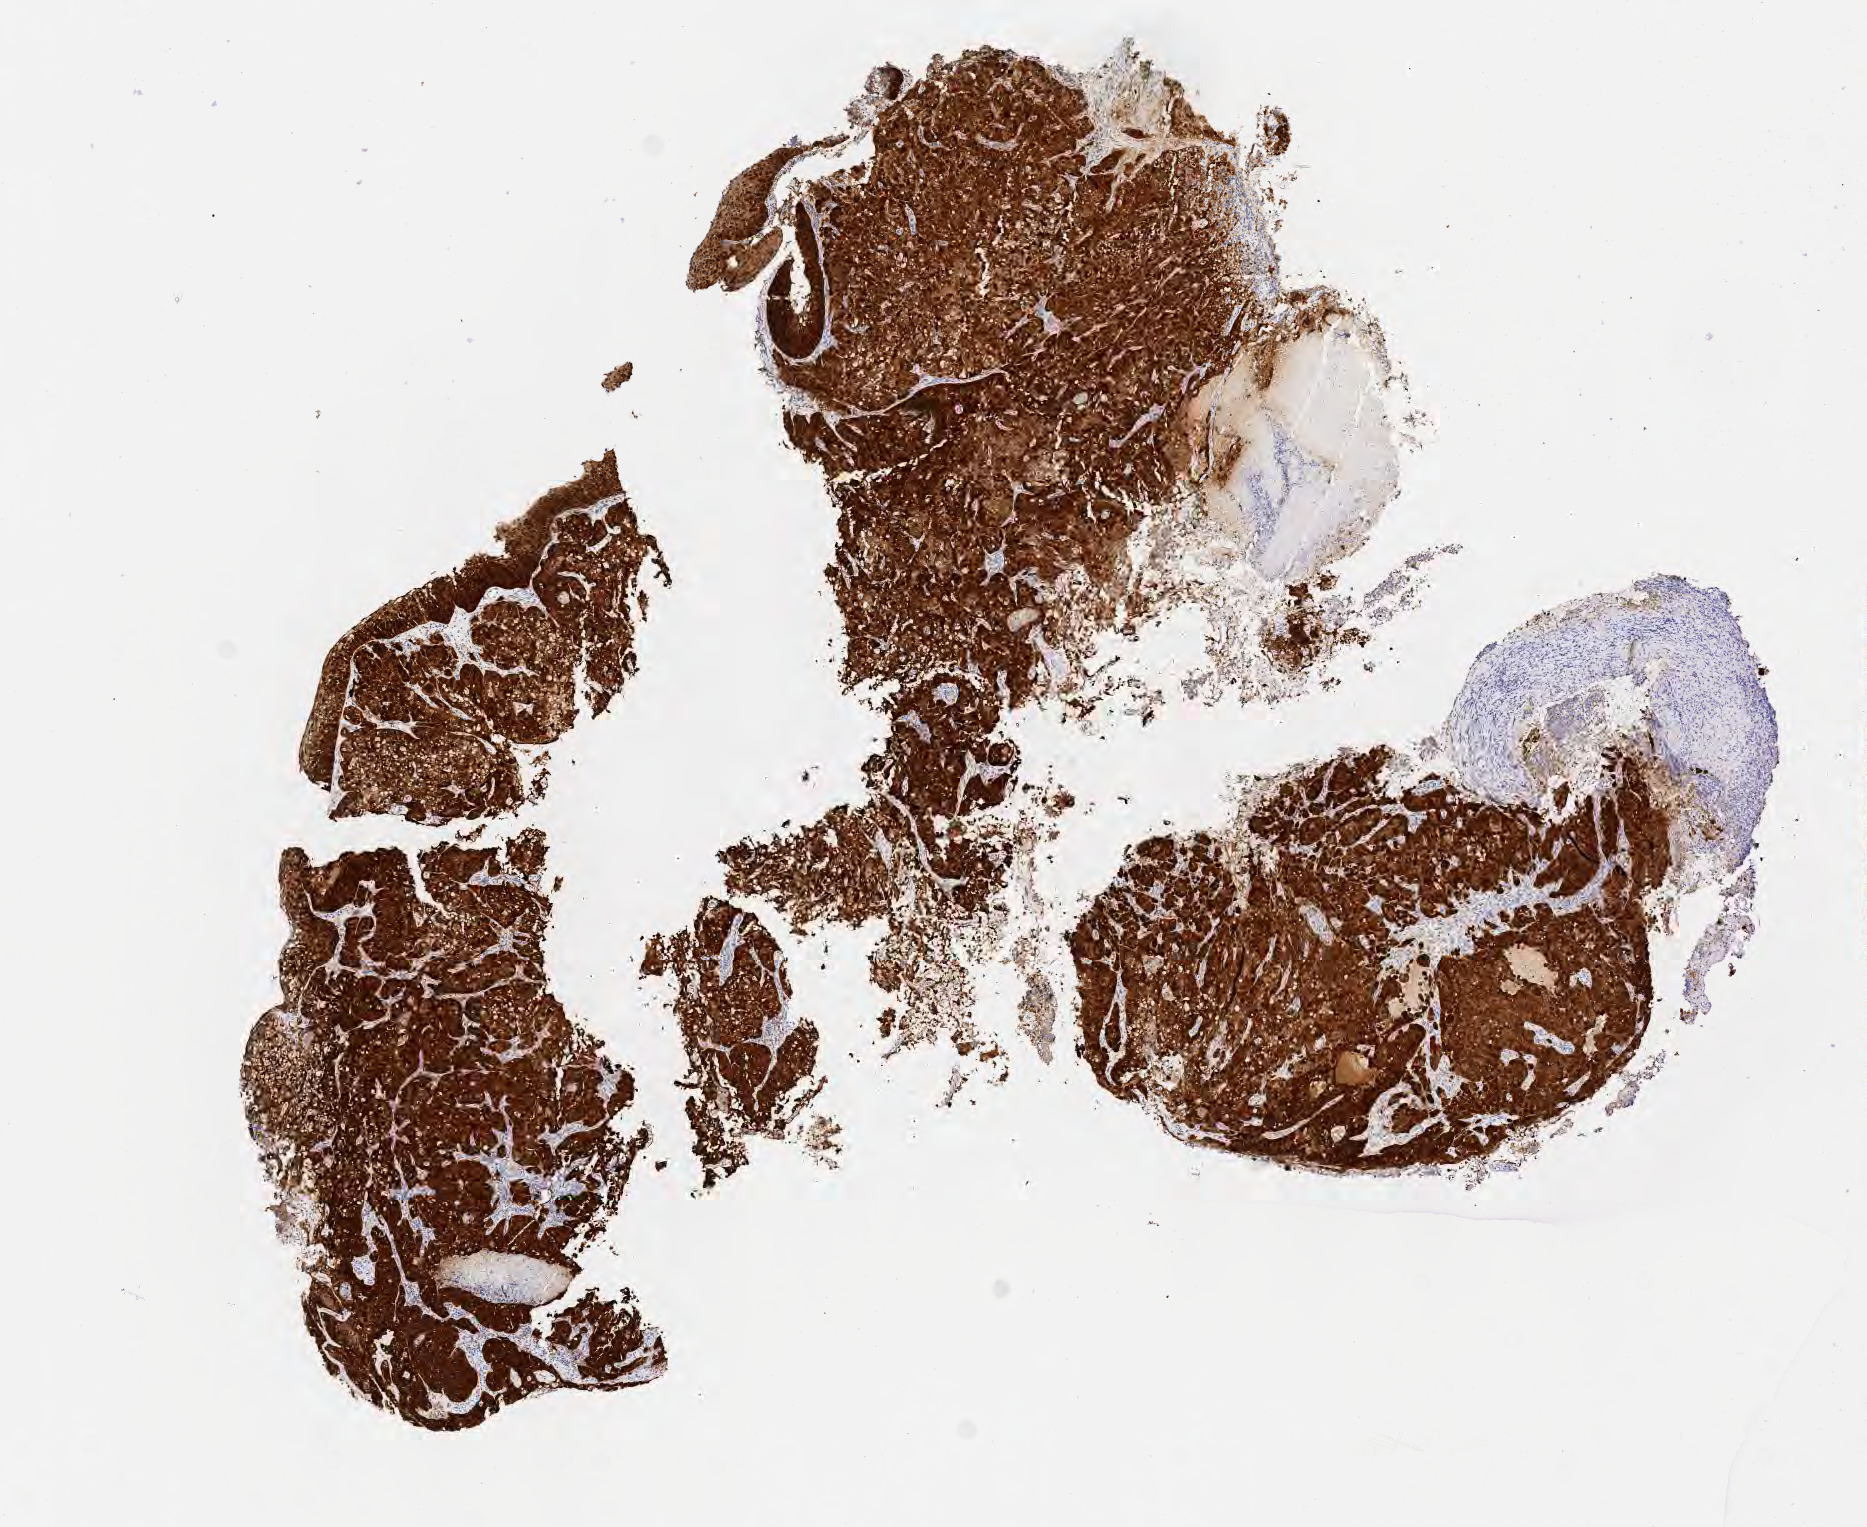
IHC for p16 (p16INK4a), whole-slide image, low-resolution overview of the scanned area, about 7.6 x 6.2 mm; tumor tissue; site: cervix. Female patient, aged 56.
• histologic diagnosis: Adenocarcinoma, NOS